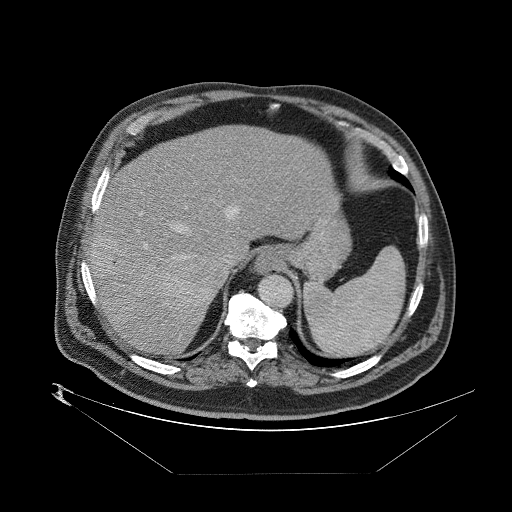
Contrast-enhanced abdominal CT (liver protocol), one axial slice; position 63 of 89 along the scan axis; reconstruction kernel STANDARD; one of 2 acquisitions stored at this slice position; soft-tissue window (W 400 / L 40 HU); 2.5 mm slice thickness; 512 × 512 image matrix. Case-level facts recorded for this patient, not image findings: diagnosis: hepatocellular carcinoma (patient treated with transarterial chemoembolisation; whether this scan precedes or follows treatment is not stated here); TNM stage (as recorded): Stage-II; Child-Pugh class: B; tumour size: 4 cm.
Annotated regions visible in this slice (semi-automatically segmented with operator editing):
- abdominal aorta: bounding box <259,276,293,309> (left, top, right, bottom; pixels)
- liver parenchyma outside the tumour (the mass and vessels are separate outlines, so this box may not span the whole liver): <90,122,342,353>
- mass: <92,237,225,325>
- liver vessels: <92,194,225,328>